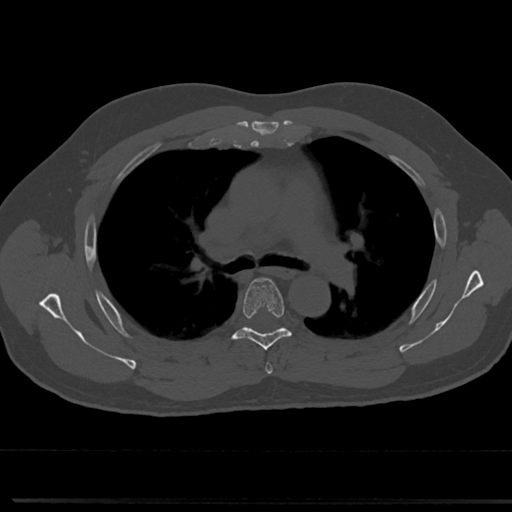
CT including the spine, one axial slice; slice 500 of 817 in the series (ordered by position); reconstruction kernel Br40s/3; bone window (W 1800 / L 400 HU); 0.5 mm slice thickness; 512 × 512 image matrix, field of view 355 × 355 mm. Patient: male, 61 years. From the clinical record (not read from this slice): primary cancer: prostate.
Outlined on this slice (semi-automatically segmented with operator editing):
- T4 vertebra: bounding box [x1, y1, x2, y2] px = [264, 353, 273, 374]
- T5 vertebra: [218, 276, 309, 352]